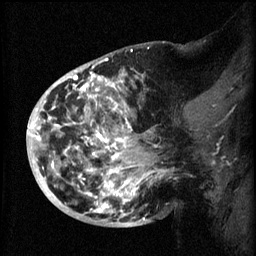
Breast MRI (dynamic contrast-enhanced), one sagittal slice; position 25 of 60 along the scan axis; 3 images stored at this slice position (order not interpretable as contrast timing); 1.5 T; TE 4.2 ms, TR 8.2 ms; 256 × 256 image matrix, field of view 200 × 200 mm. Patient: female, 50 years.
Structures marked on this image (semi-automatically segmented with operator editing):
- analysis volume of interest (the breast-tissue region the enhancement analysis was run in; not a lesion): bounding box (x1, y1, x2, y2) in pixels: (44, 72, 173, 219)
- tumour enhancement mask (voxels above the 70 % enhancement threshold inside the analysis volume of interest): (47, 72, 167, 219)